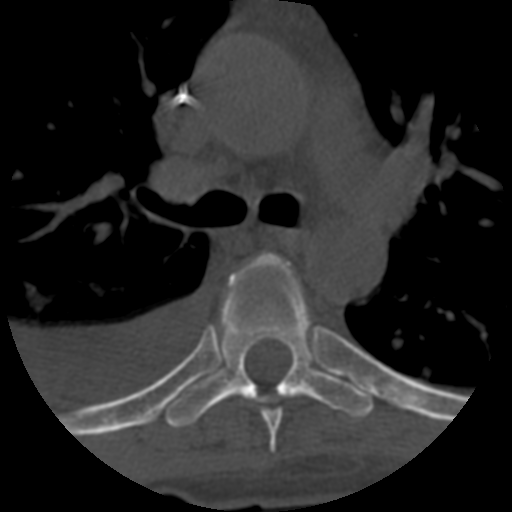
CT including the spine, one axial slice; position 442 of 708 along the scan axis; 120 kVp; one of 3 acquisitions stored at this slice position; bone window (W 1800 / L 400 HU); 512 × 512 image matrix, field of view 160 × 160 mm. Patient age 55 years. Case-level facts recorded for this patient, not image findings: primary cancer: colon.
Annotated regions visible in this slice (semi-automatically segmented with operator editing):
- T5 vertebra: bounding box (x1, y1, x2, y2) in pixels: (263, 410, 282, 453)
- T6 vertebra: (165, 252, 374, 428)